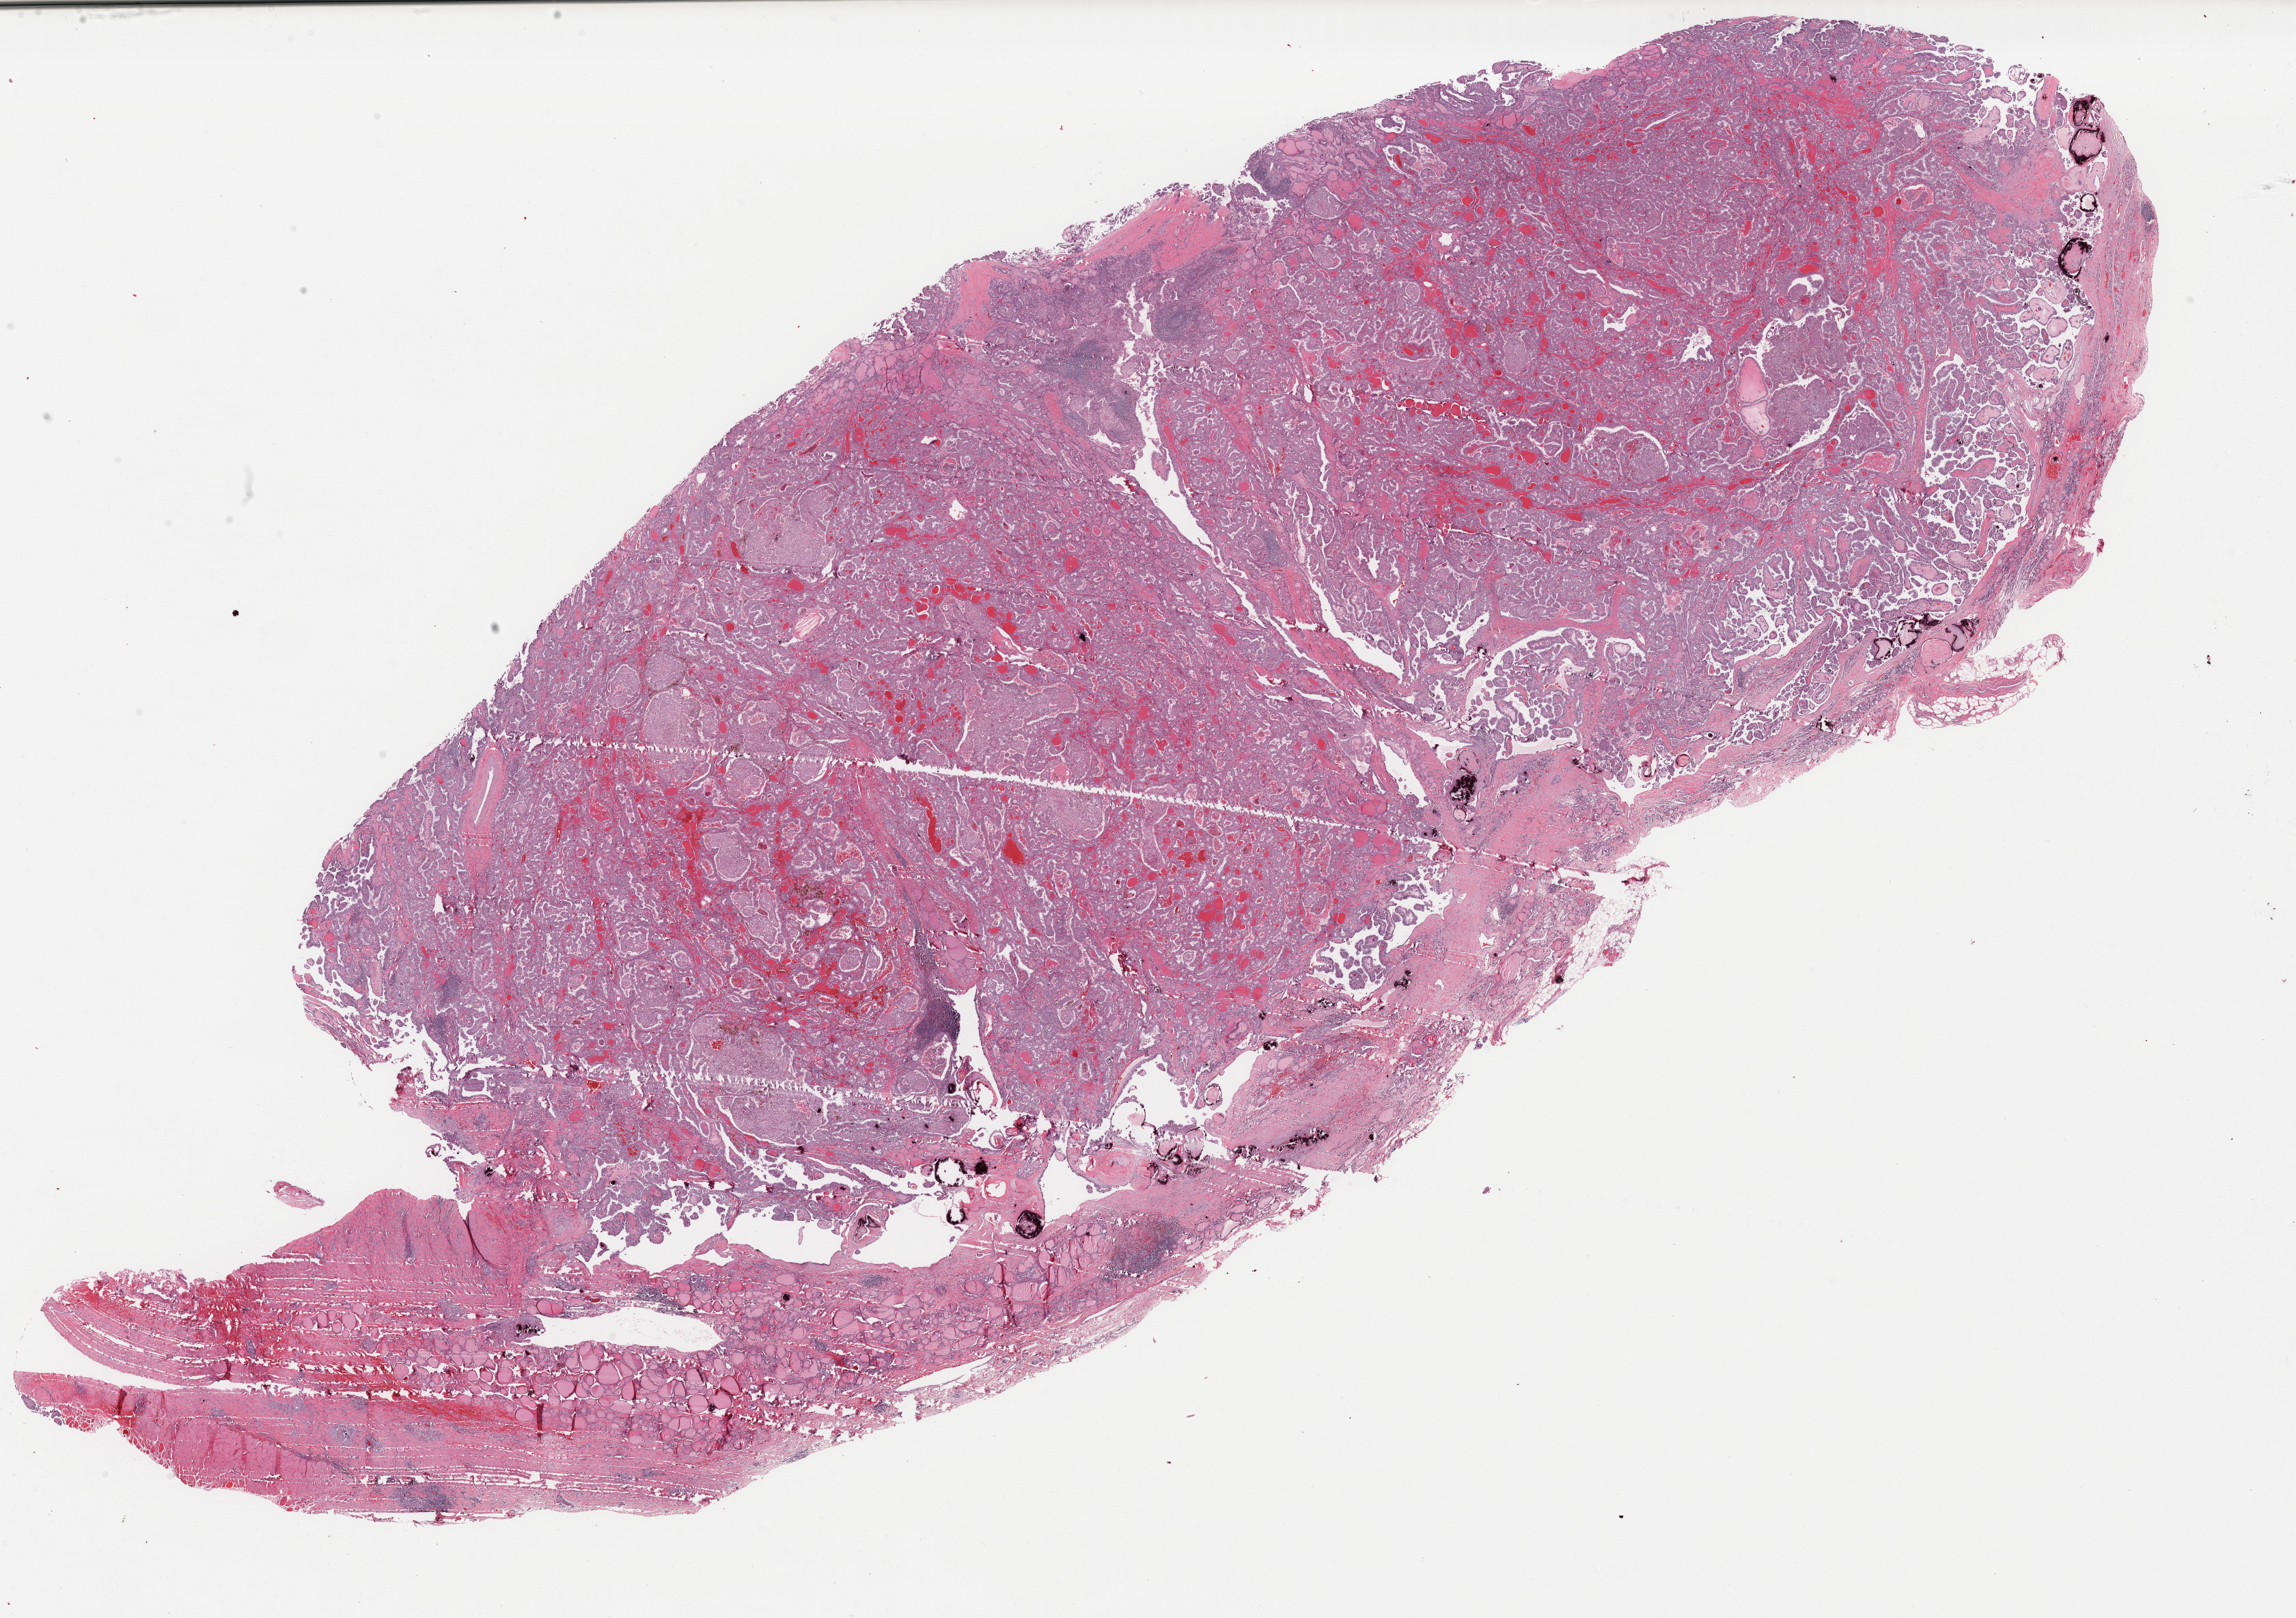
H&E whole-slide image — low-resolution overview of the scanned area, about 26.5 x 18.7 mm (slide scanned at 40x); FFPE section; thyroid, primary tumour sample. Patient: male, age at initial diagnosis 55 years.
- pathologic diagnosis: Papillary adenocarcinoma, NOS (thyroid gland)
- AJCC pathologic stage: IVA (7th edition)
- TNM: T3 N1b M0